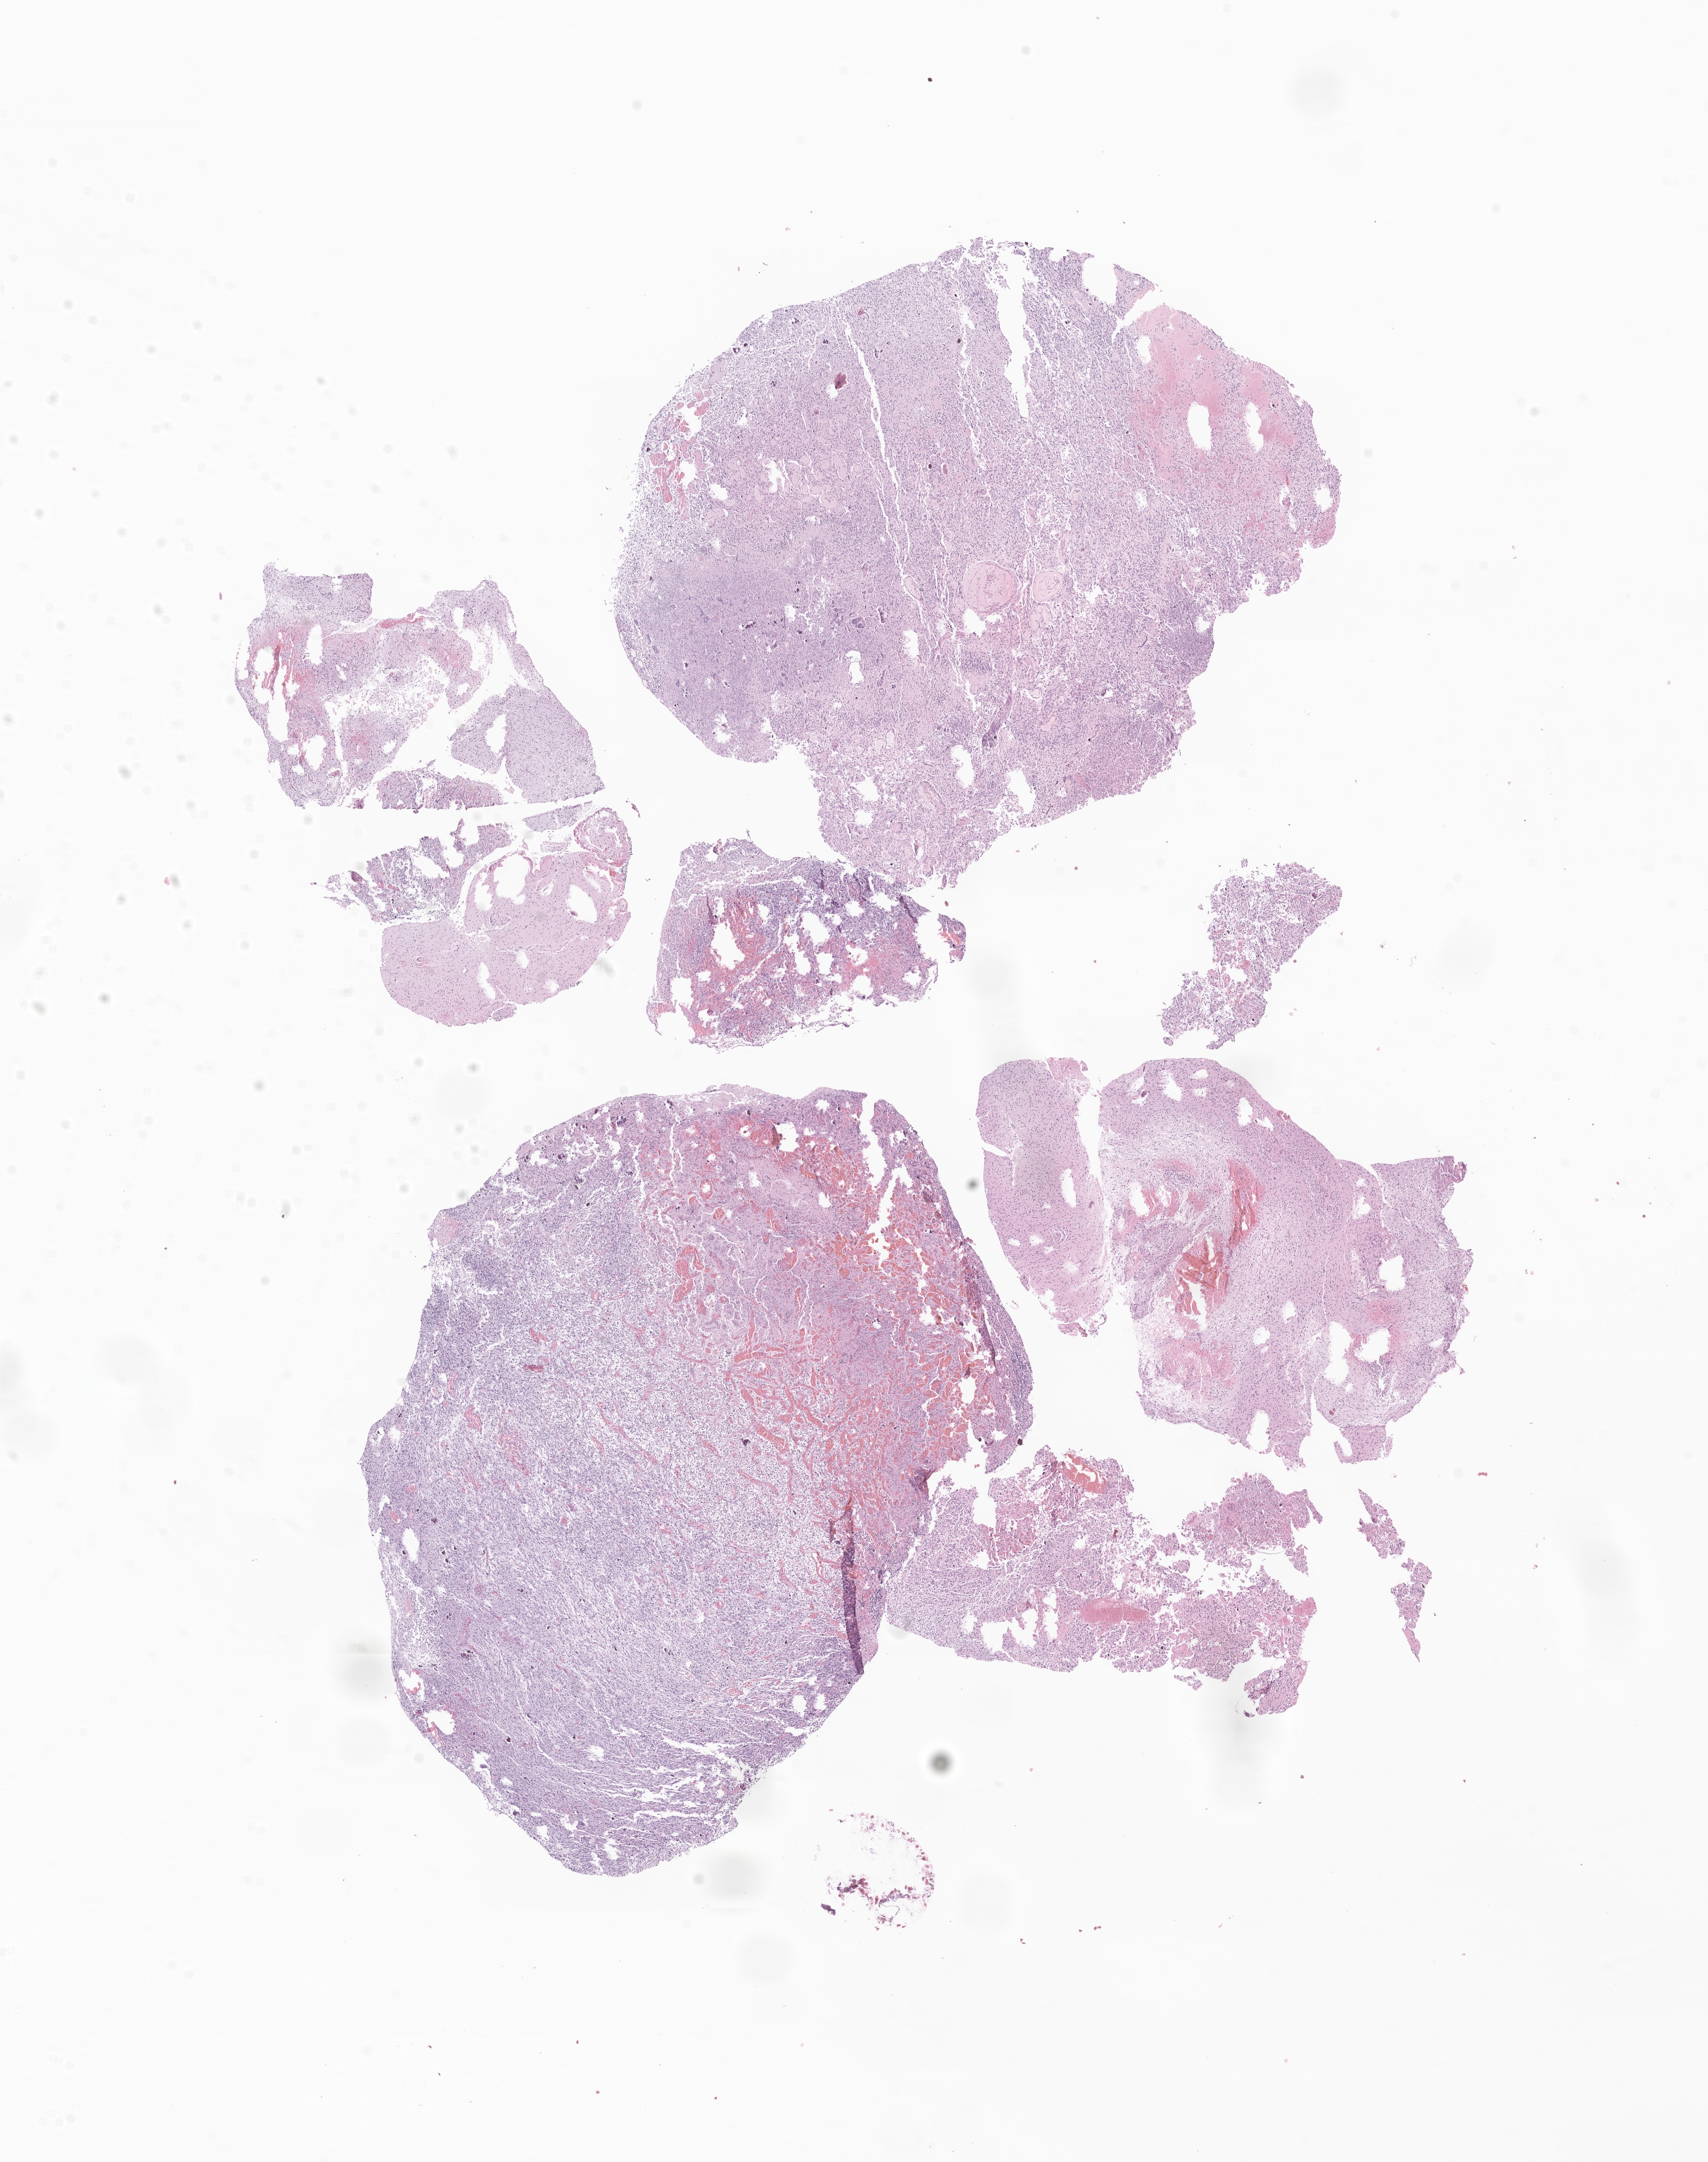
Haematoxylin and eosin whole-slide image of tumor tissue from the brain, whole scanned area (about 14.3 x 18.1 mm) shown as a low-resolution overview. Formalin-fixed paraffin-embedded section. Patient male; age 122 months.
Diagnosis (ICD-O-3 morphology term): Neoplasm, malignant.